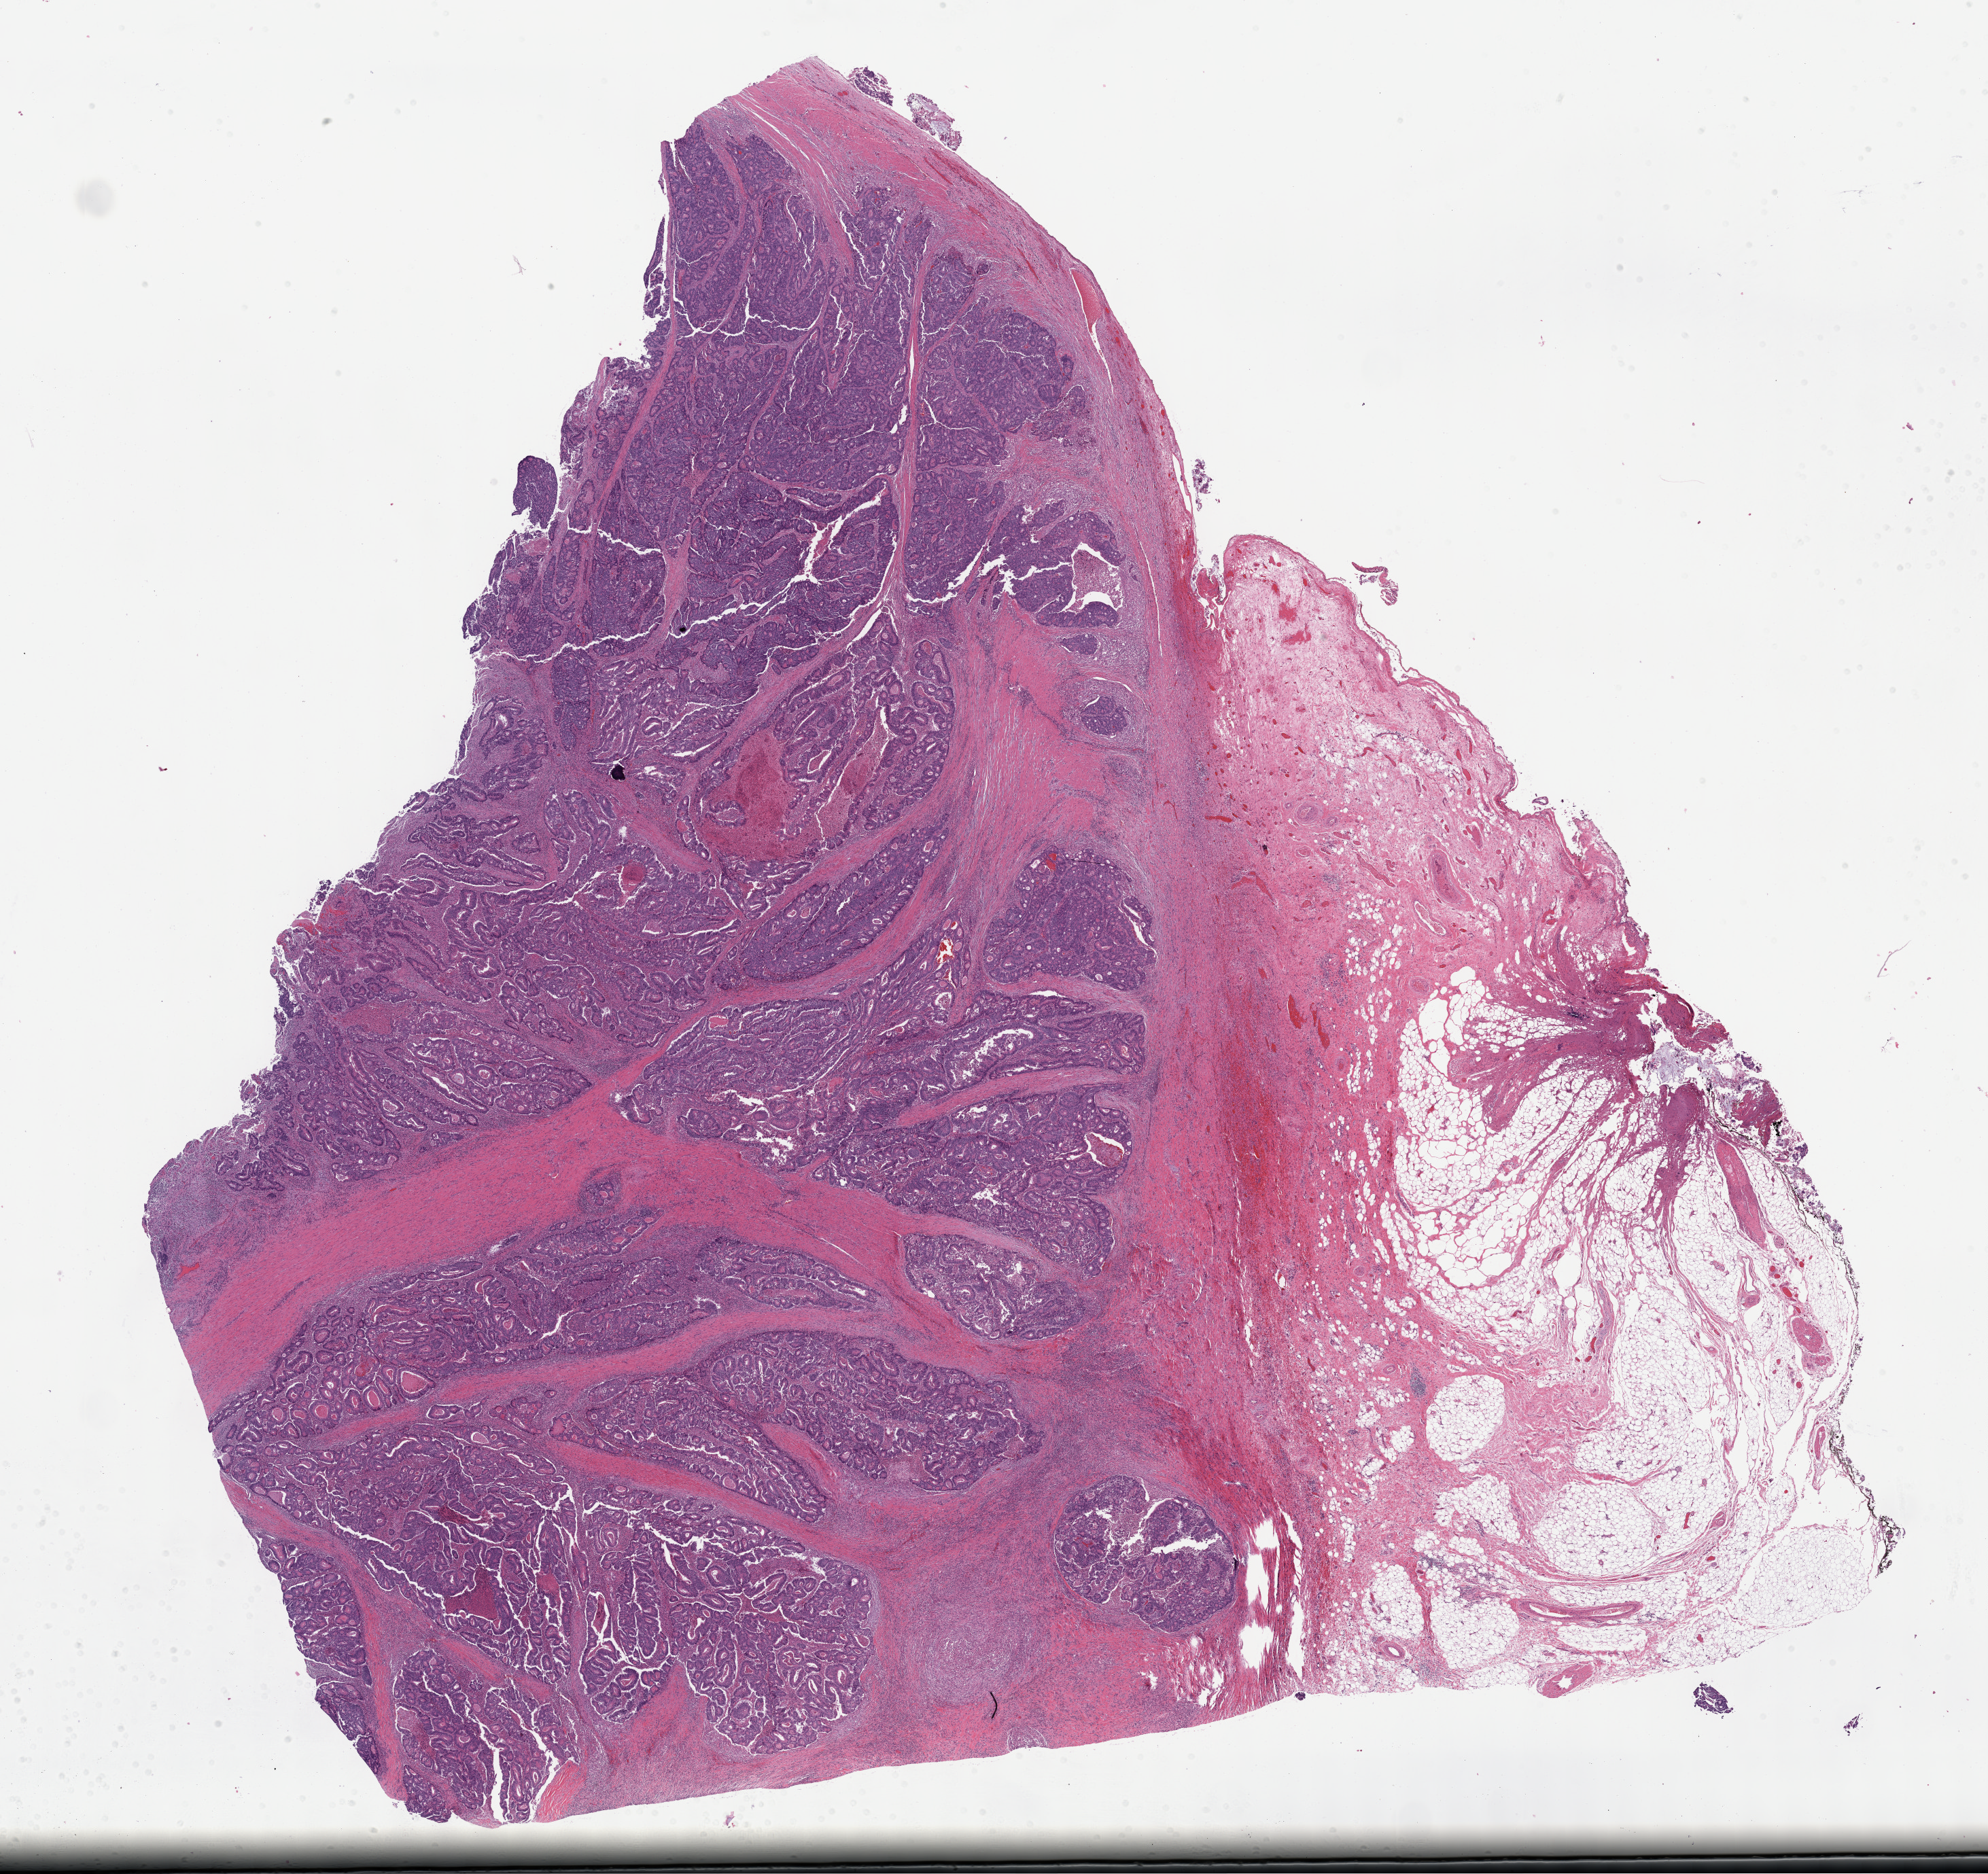
H&E whole-slide image — shown as a low-resolution overview of the whole scanned area (about 23.7 x 22.3 mm, acquisition: 40x scan); FFPE section; colon, primary tumour sample. Female patient; age at initial diagnosis 84 years.
Diagnosis: Adenocarcinoma, NOS (ascending colon). AJCC pathologic stage: I (7th edition).